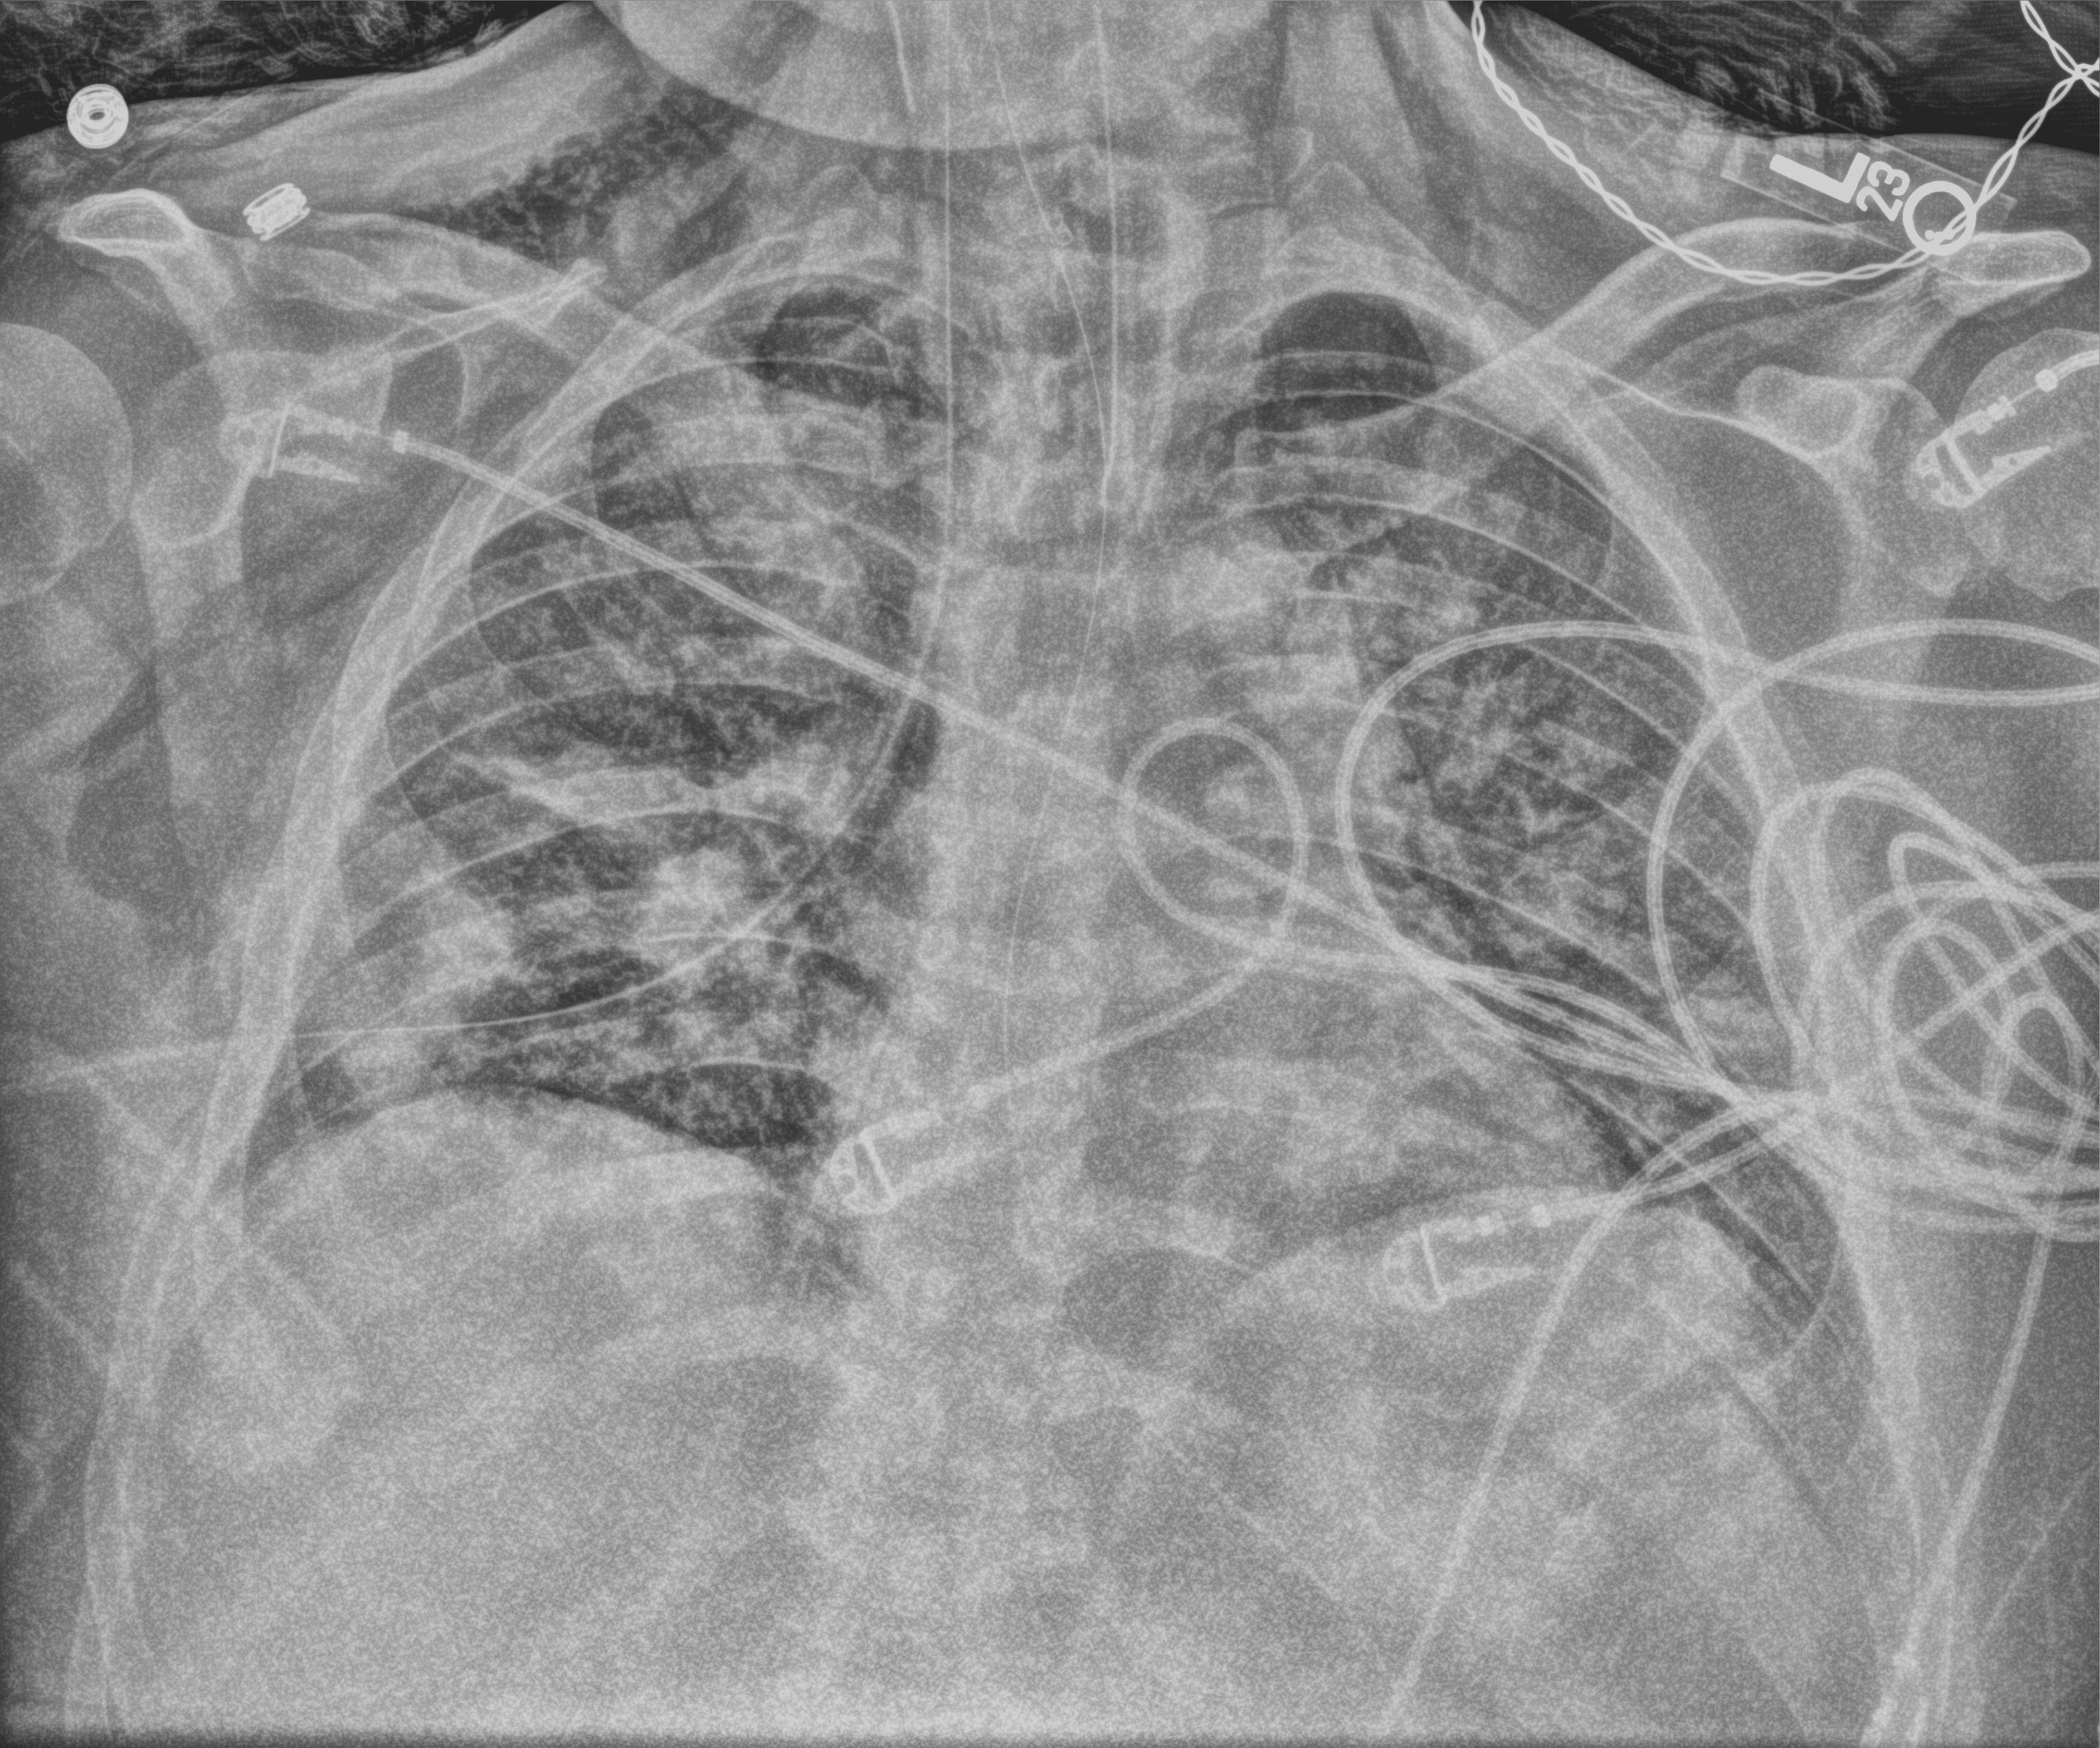
Bedside chest radiograph (computed radiography); anteroposterior (AP) projection. Patient hospitalised with COVID-19, aged 18–59 years.
From the hospital-stay record, not from the radiograph (when in the stay this image was taken is not recorded): mechanically ventilated during this hospital stay: yes; admitted to intensive care during this hospital stay: yes.